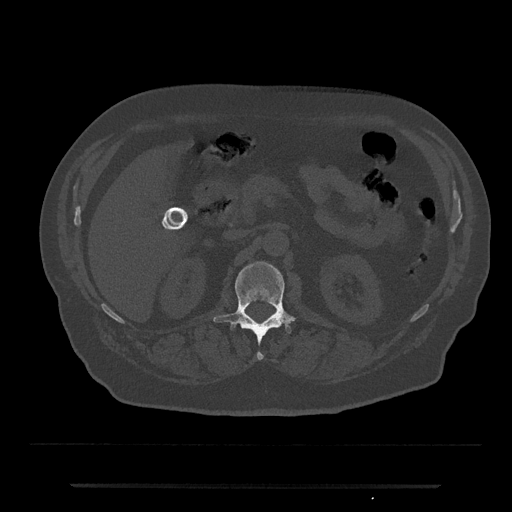
CT including the spine, one axial slice; slice 534 of 797 in the series (ordered by position); reconstruction kernel Br40s/3; 120 kVp; bone window (W 1800 / L 400 HU); 0.5 mm slice thickness; 512 × 512 image matrix. Patient: male, 80 years. Case-level facts recorded for this patient, not image findings: primary cancer: prostate.
Annotated regions visible in this slice (semi-automatic segmentation, software-assisted and operator-edited):
- L1 vertebra: bounding box [x1, y1, x2, y2] px = [214, 261, 295, 360]